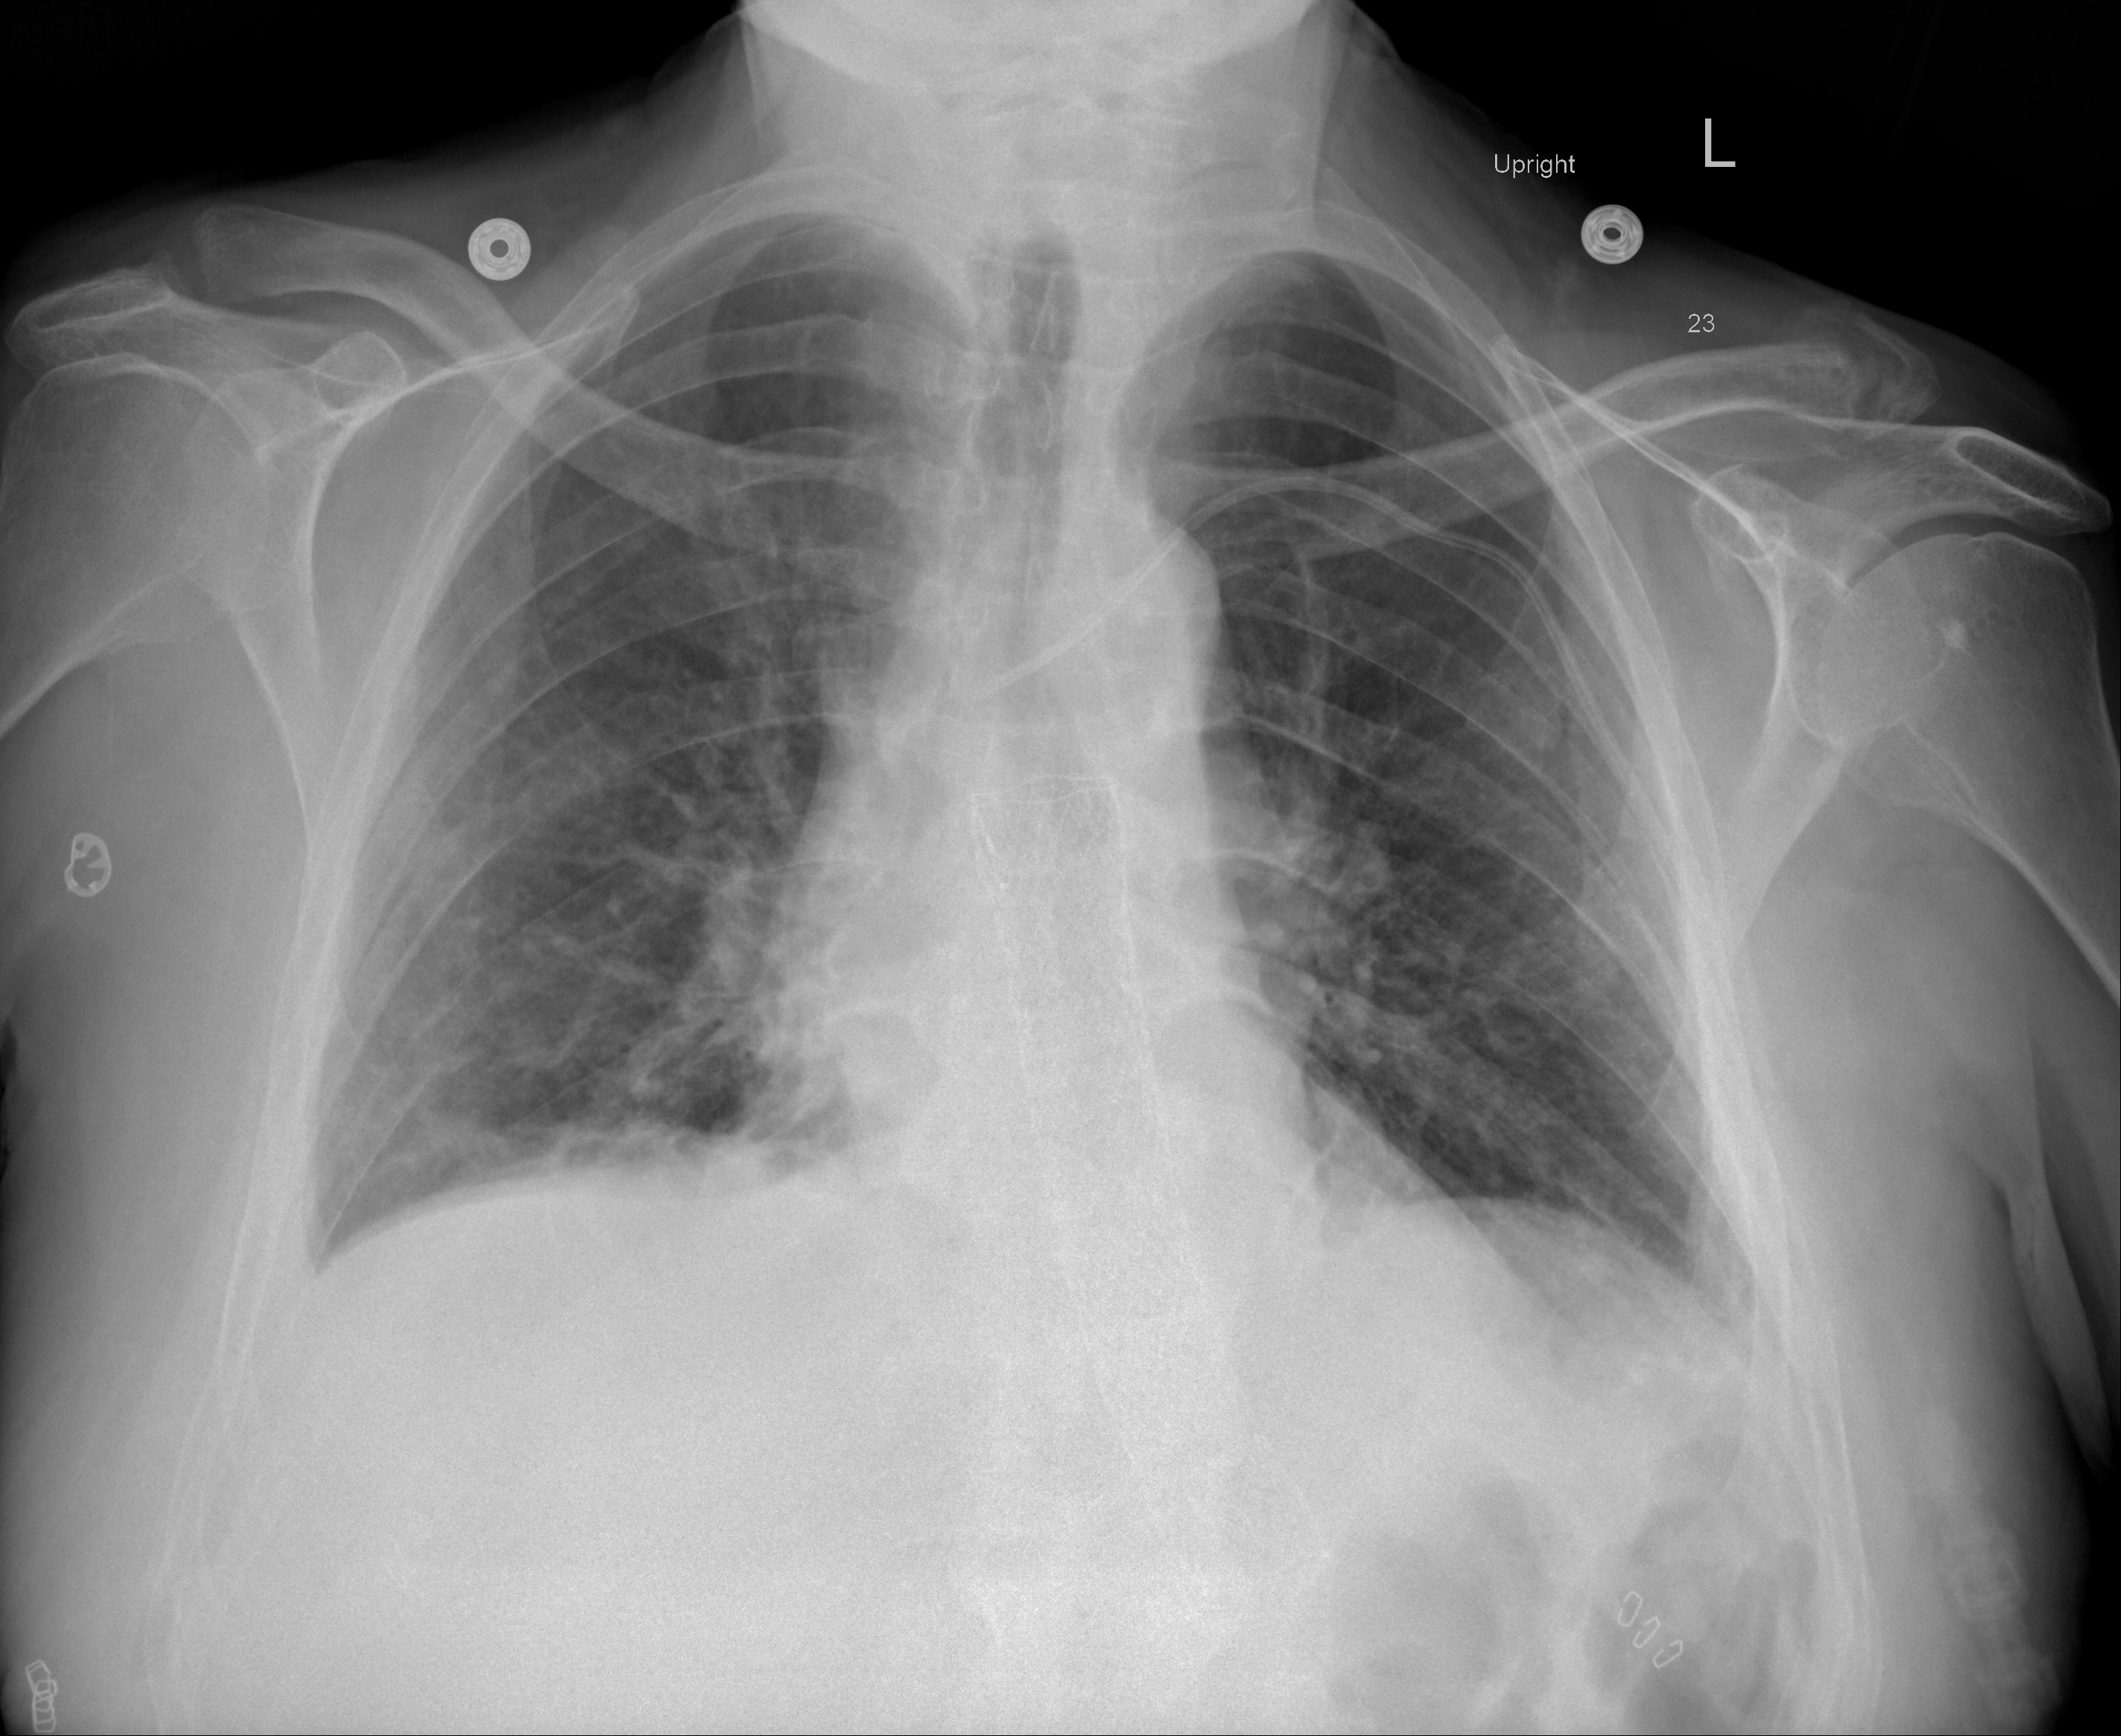
Chest X-ray (portable), AP projection. Male patient, age 64 years; COVID-19 (test-positive).
Key findings recorded by the radiologist: Bibasilar atelectasis and small bilateral effusions are again noted.